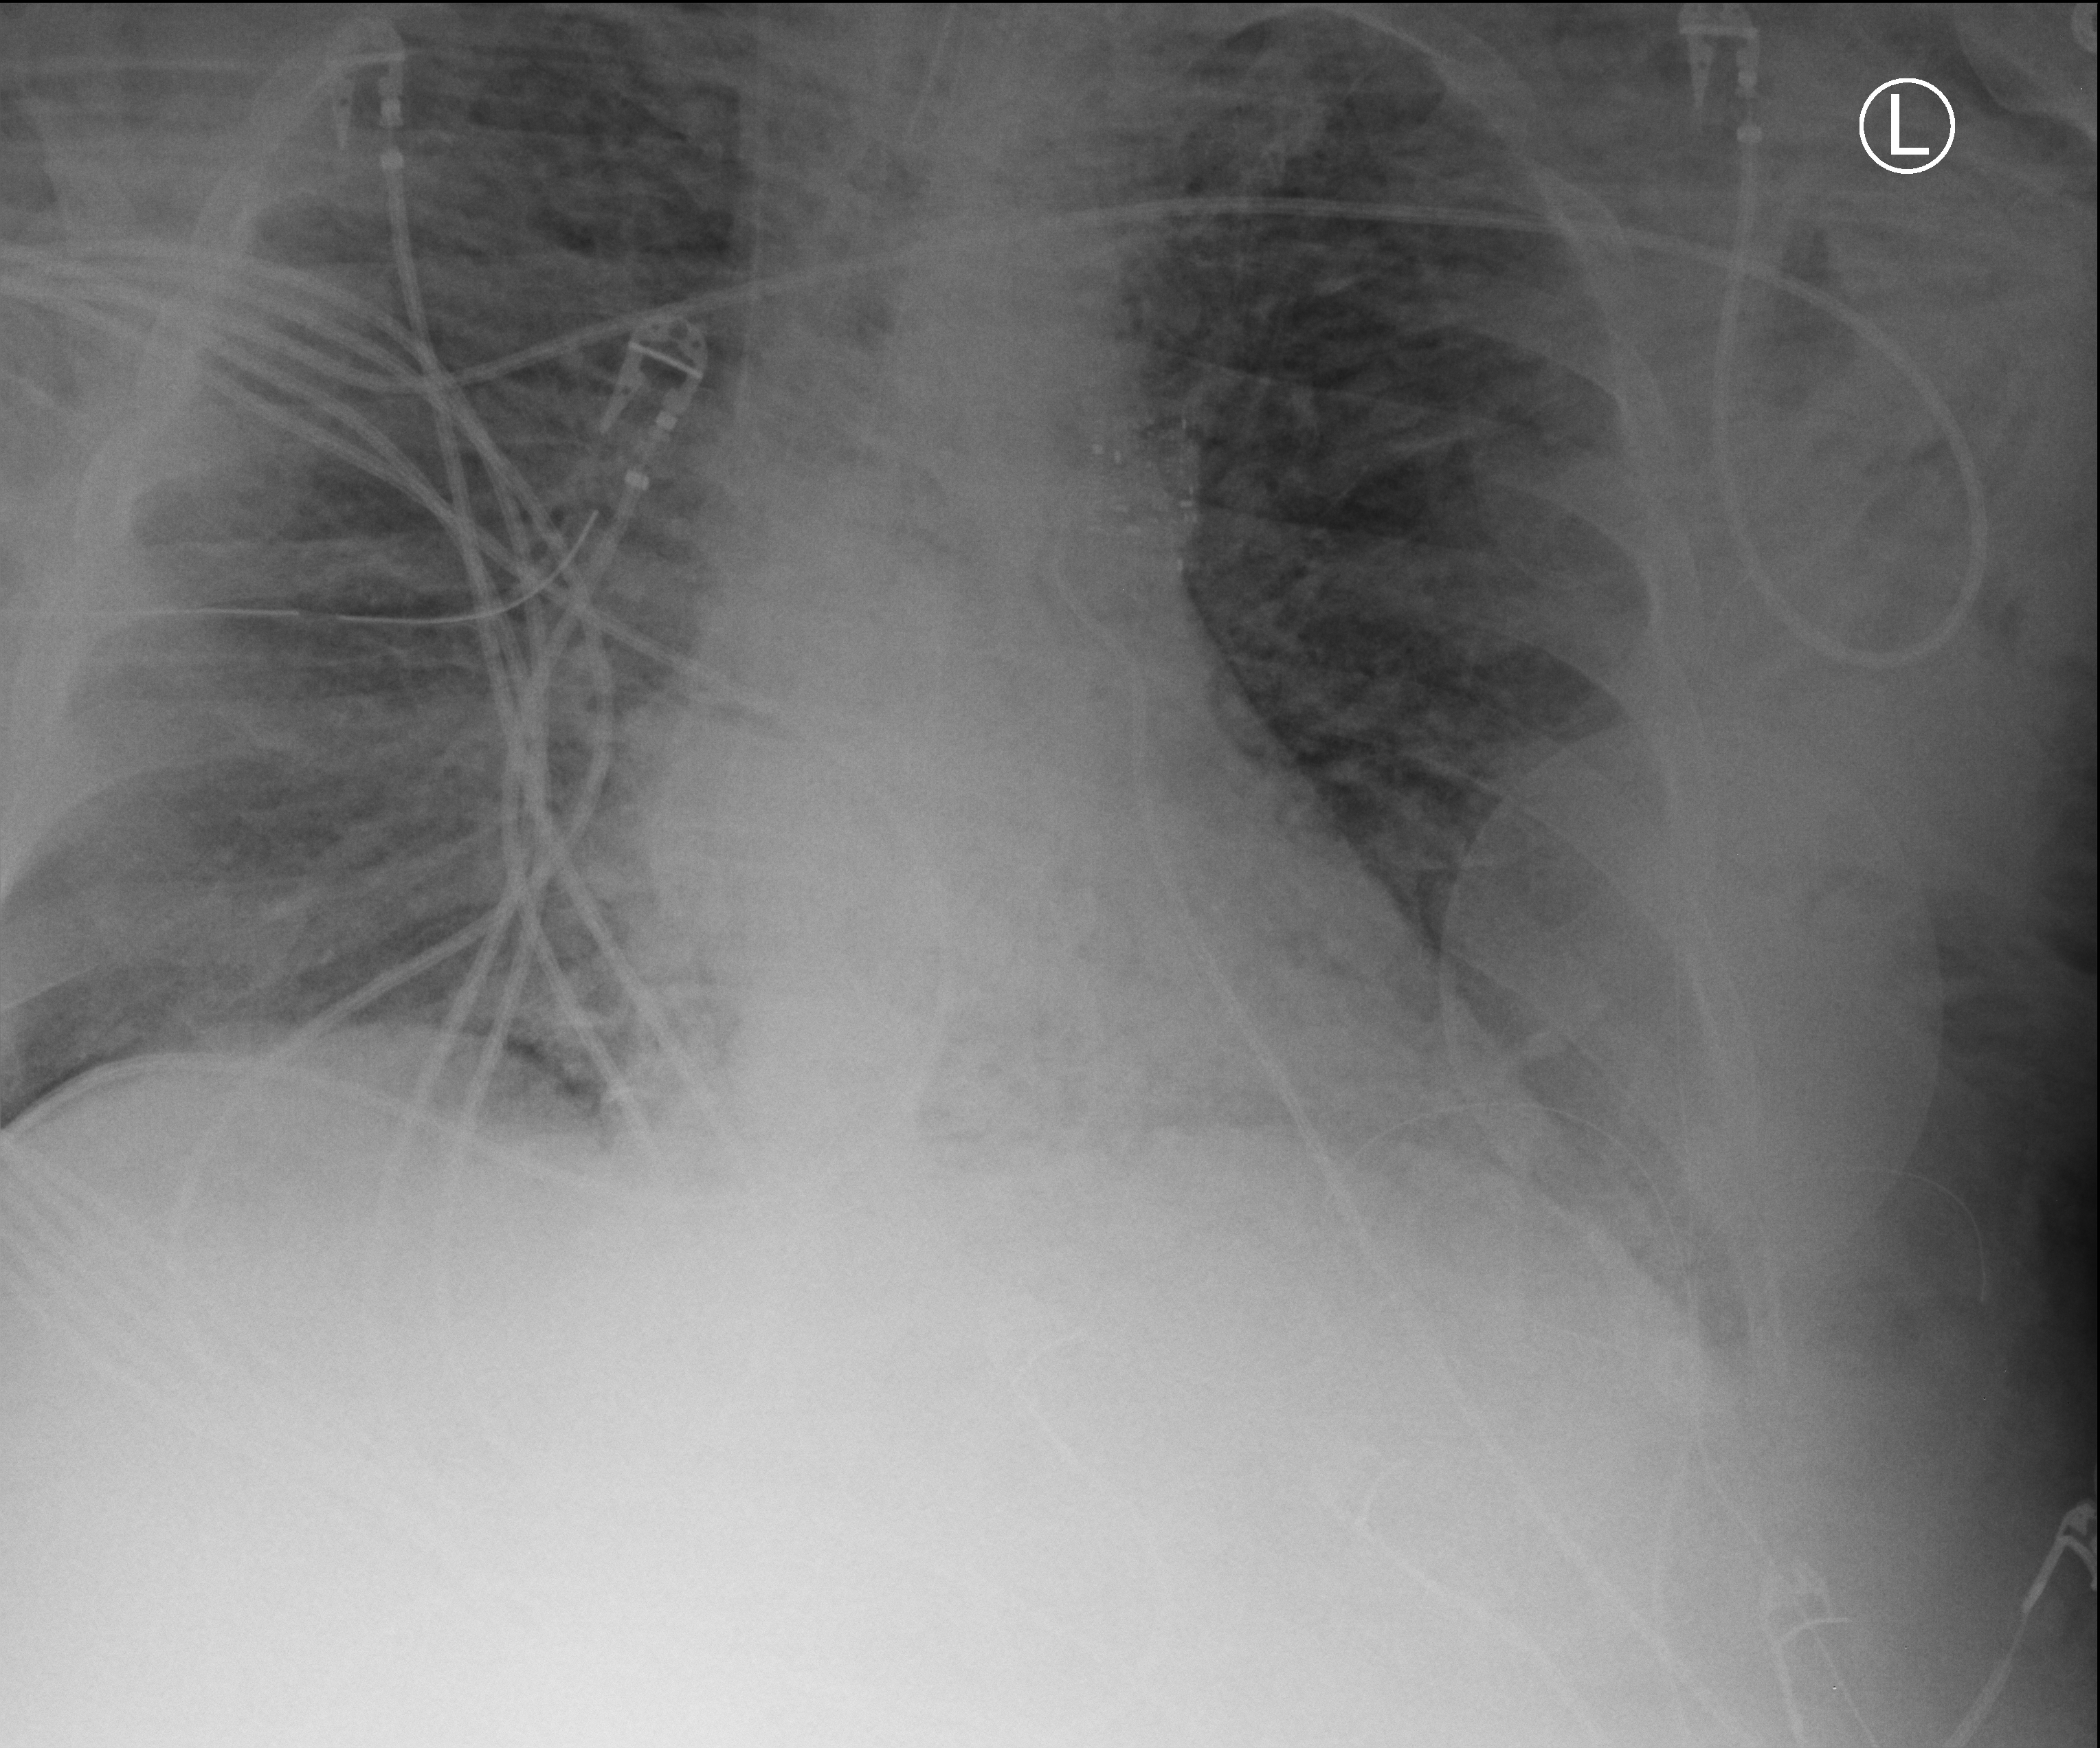
Chest X-ray (portable); anteroposterior (AP) projection. Patient hospitalised with COVID-19, aged 18–59 years.
Hospital-stay facts (about this admission, not read from this image; timing relative to this image not recorded): admitted to intensive care during this hospital stay: yes.